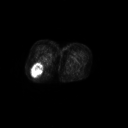
FDG PET of an extremity soft-tissue mass (from a PET/CT study), one axial slice. Slice 32 of 267 in the series (ordered by position). 3.27 mm slice thickness. 128 × 128 image matrix, field of view 700 × 700 mm. Patient: female, 70 years. From the clinical record (not read from this slice): histological type: synovial sarcoma; grade: intermediate; site of the primary tumour: right buttock.
Annotated regions visible in this slice (expert contour drawn on MRI and transferred to this co-registered scan by the dataset authors):
- gross tumour volume including surrounding oedema: bounding box [x1, y1, x2, y2] px = [31, 61, 43, 76]
- gross tumour volume (mass): [31, 62, 42, 76]